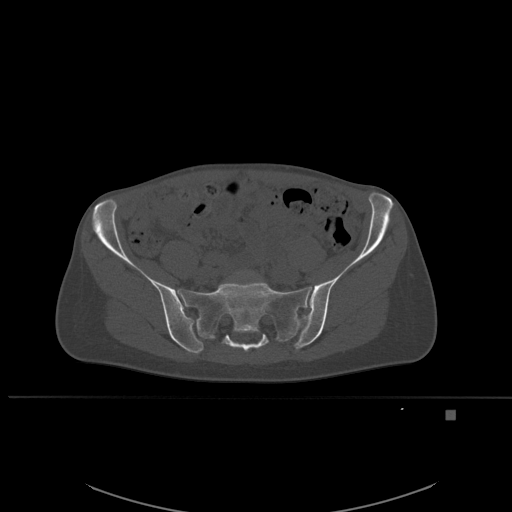
CT including the spine, one axial slice. Slice 153 of 537 in the series (ordered by position). Bone window (W 1800 / L 400 HU). 1.5 mm slice thickness. 512 × 512 image matrix. Patient: female, 45 years. Case-level facts recorded for this patient, not image findings: primary cancer: lung.
Annotated regions visible in this slice (semi-automatic segmentation, software-assisted and operator-edited):
- L5 vertebra: bounding box (x1, y1, x2, y2) in pixels: (237, 270, 254, 276)